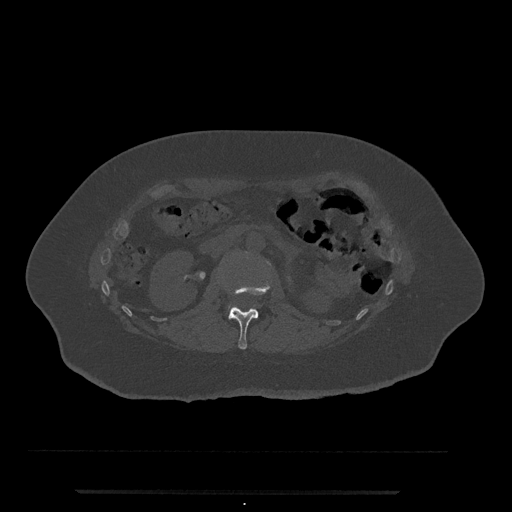
CT including the spine, one axial slice; position 81 of 797 along the scan axis; reconstruction kernel Br40s/3; 120 kVp; bone window (W 1800 / L 400 HU); 0.5 mm slice thickness; 512 × 512 image matrix, field of view 440 × 440 mm. Patient: female, 51 years. From the clinical record (not read from this slice): primary cancer: neuro; vertebrae with lytic lesions (as recorded): T8.
Annotated regions visible in this slice (semi-automatically segmented with operator editing):
- L1 vertebra: bounding box [x1, y1, x2, y2] px = [225, 278, 272, 350]
- L2 vertebra: [228, 306, 238, 312]